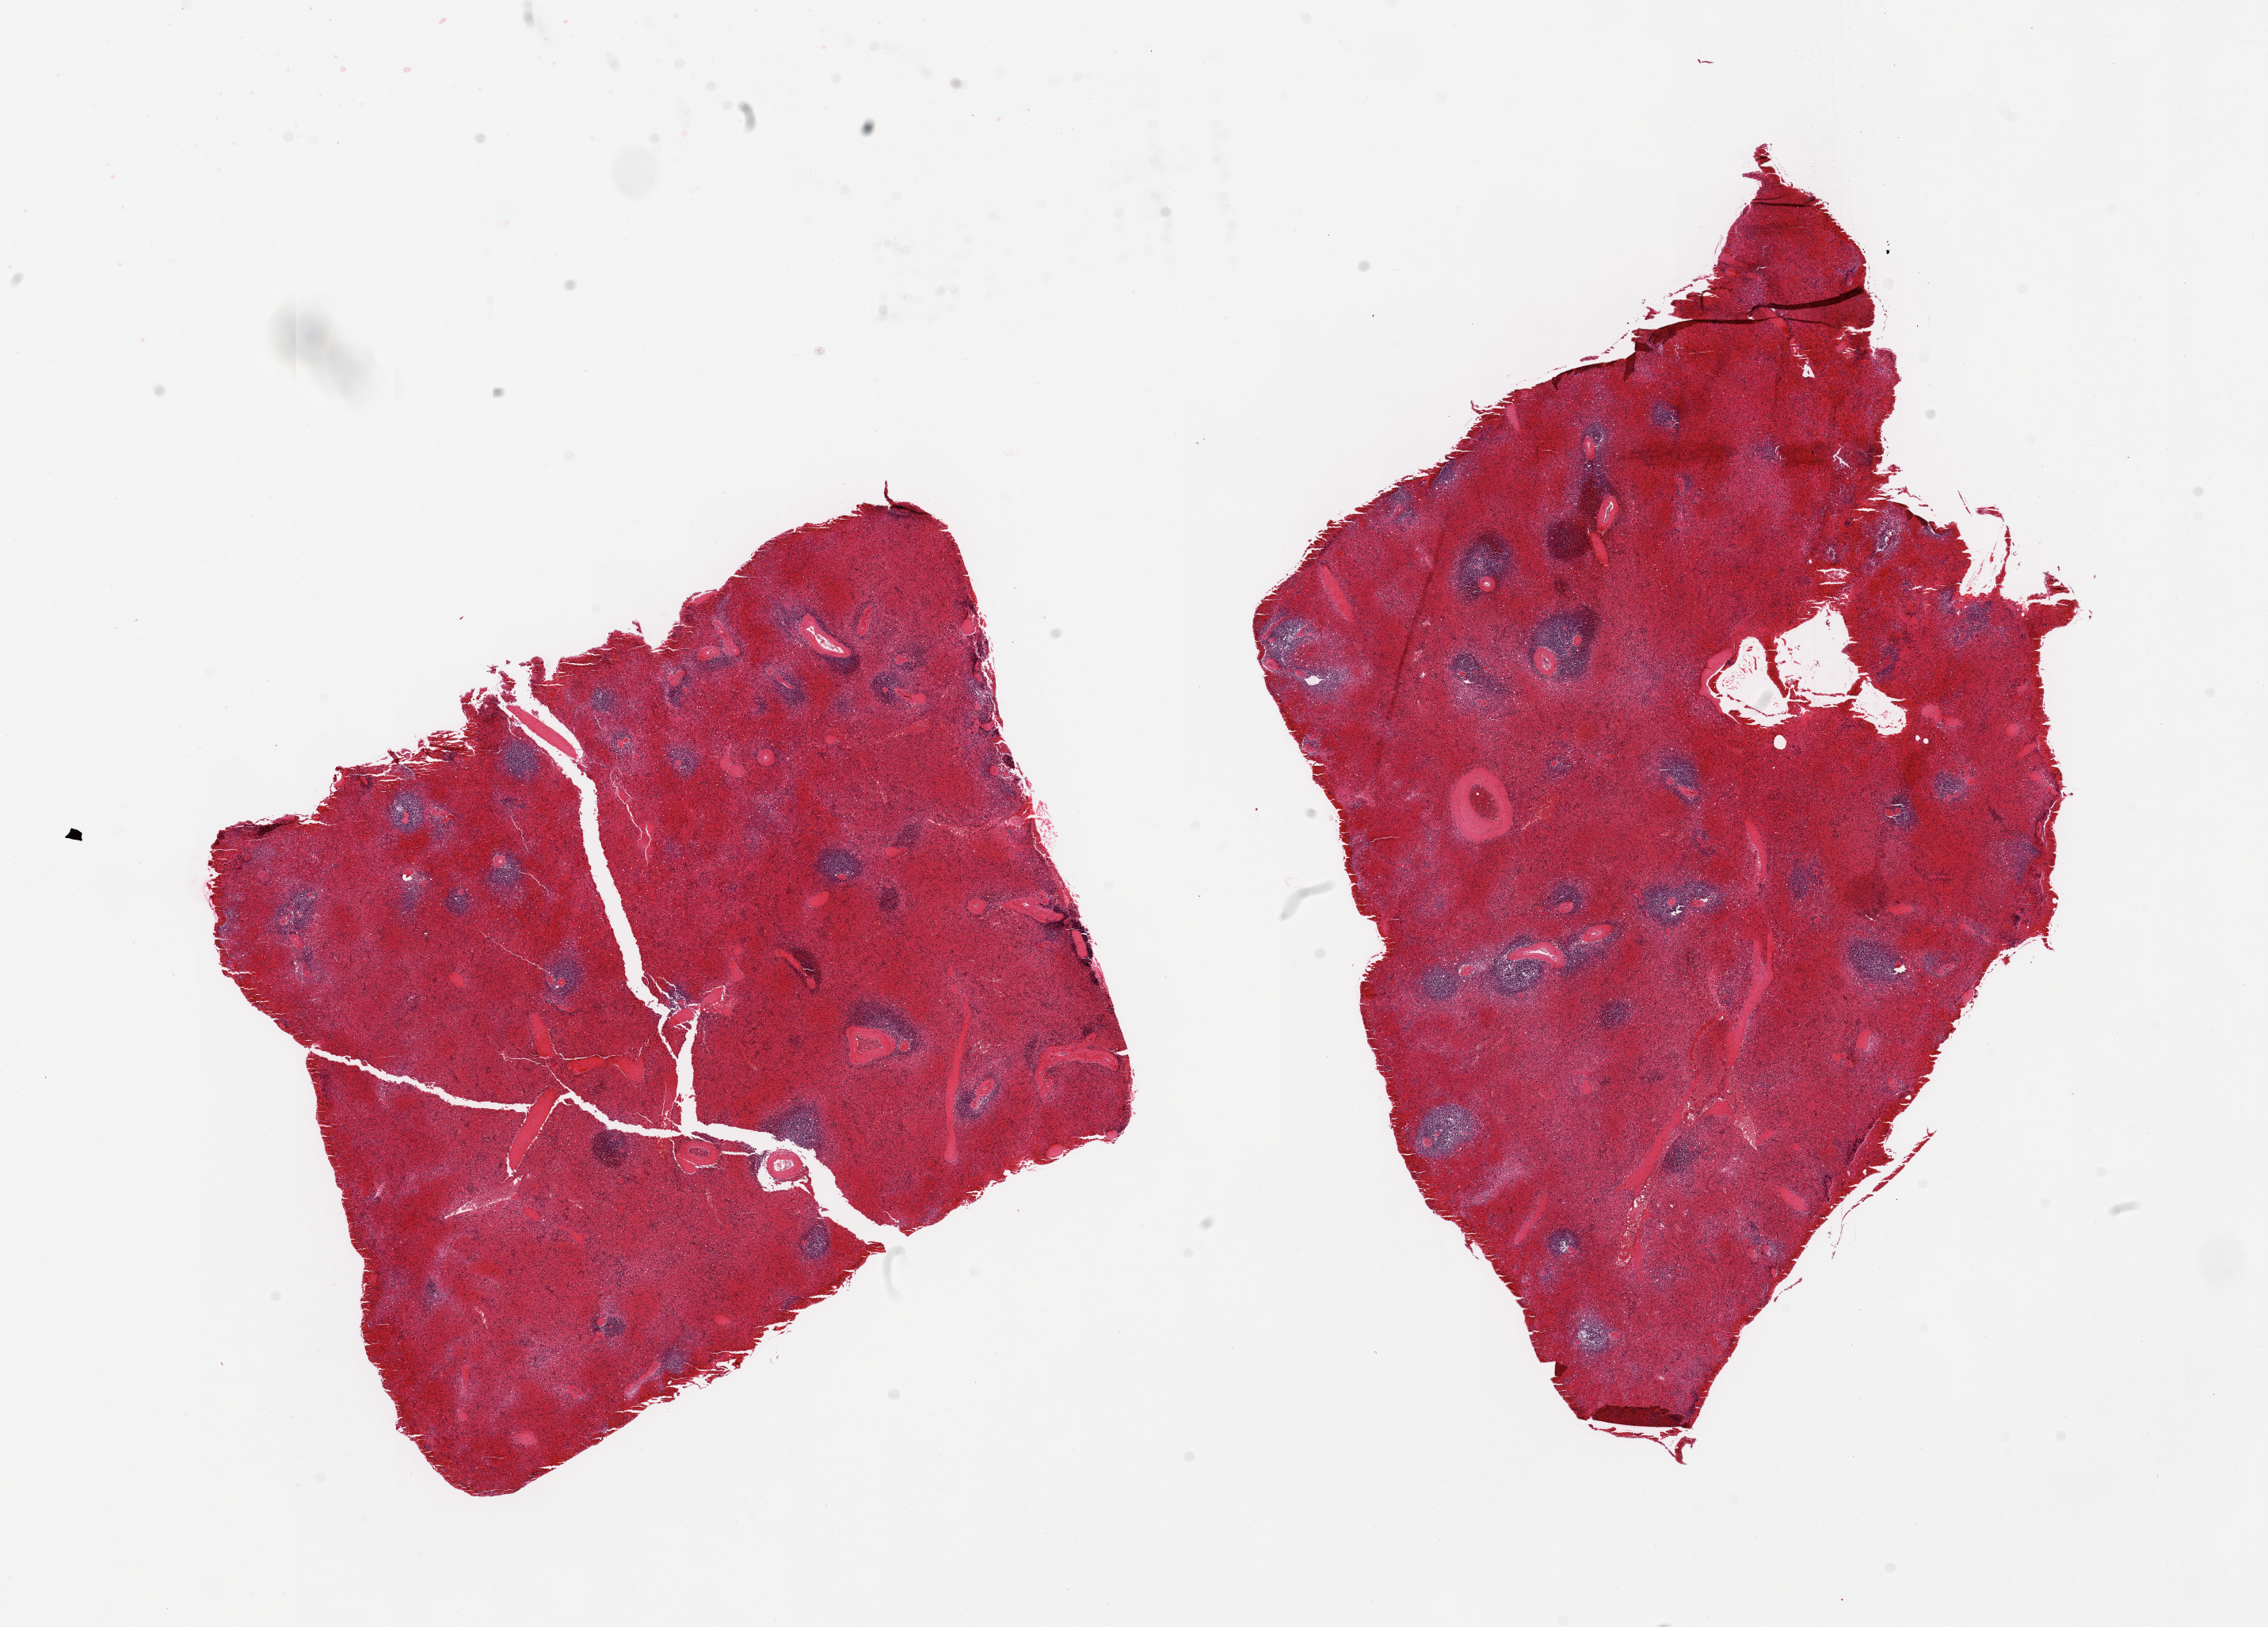
Whole-slide image, hematoxylin and eosin (H&E) stain, whole scanned area (about 22.6 x 16.2 mm, from a 20x scan) shown as a low-resolution overview, PAXgene-fixed paraffin-embedded (PFPE) section, sampled site (target tissue): spleen, donor tissue sample. Donor: male.
Pathologist's review note for this sample: 2 pieces; severe vascular congestion.